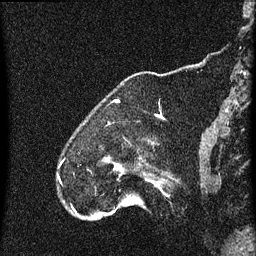
Breast MRI (dynamic contrast-enhanced), one sagittal slice. Position 9 of 60 along the scan axis. Dynamic contrast-enhanced series, image 2 of 4 at this slice position (ordered by acquisition). 1.5 T. TE 4.2 ms, TR 8 ms. 2 mm slice thickness. 256 × 256 image matrix, field of view 180 × 180 mm. Patient: female, 52 years.
Annotated regions visible in this slice (semi-automatically segmented with operator editing):
- analysis volume of interest (the breast-tissue region the enhancement analysis was run in; not a lesion): bounding box (x1, y1, x2, y2) in pixels: (75, 156, 169, 219)
- tumour enhancement mask (voxels above the 70 % enhancement threshold inside the analysis volume of interest): (107, 160, 120, 167)